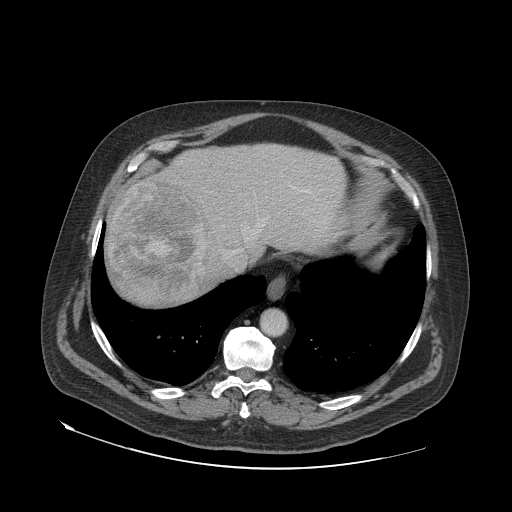
Contrast-enhanced abdominal CT (liver protocol), one axial slice. Position 62 of 79 along the scan axis. Reconstruction kernel STANDARD. Soft-tissue window (W 400 / L 40 HU). 2.5 mm slice thickness. 512 × 512 image matrix. Case-level facts recorded for this patient, not image findings: diagnosis: hepatocellular carcinoma (patient treated with transarterial chemoembolisation; whether this scan precedes or follows treatment is not stated here); TNM stage (as recorded): Stage-IVA; Child-Pugh class: A; tumour differentiation: well differentiated; tumour nodularity: multinodular.
Structures marked on this image (semi-automatically segmented with operator editing):
- abdominal aorta: bounding box <261,311,286,335> (left, top, right, bottom; pixels)
- liver parenchyma outside the tumour (the mass and vessels are separate outlines, so this box may not span the whole liver): <104,144,348,304>
- mass: <110,179,209,303>
- liver vessels: <233,187,311,254>